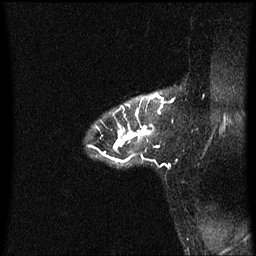
Breast MRI (dynamic contrast-enhanced), one sagittal slice; slice 48 of 60 in the series (ordered by position); dynamic contrast-enhanced series, image 2 of 3 at this slice position (ordered by acquisition); 1.5 T; TE 4.2 ms, TR 8.4 ms; 256 × 256 image matrix, field of view 200 × 200 mm. Female patient, age 32 years.
Outlined on this slice (semi-automatic segmentation, software-assisted and operator-edited):
- analysis volume of interest (the breast-tissue region the enhancement analysis was run in; not a lesion): bounding box <97,92,161,165> (left, top, right, bottom; pixels)
- tumour enhancement mask (voxels above the 70 % enhancement threshold inside the analysis volume of interest): <105,94,158,155>